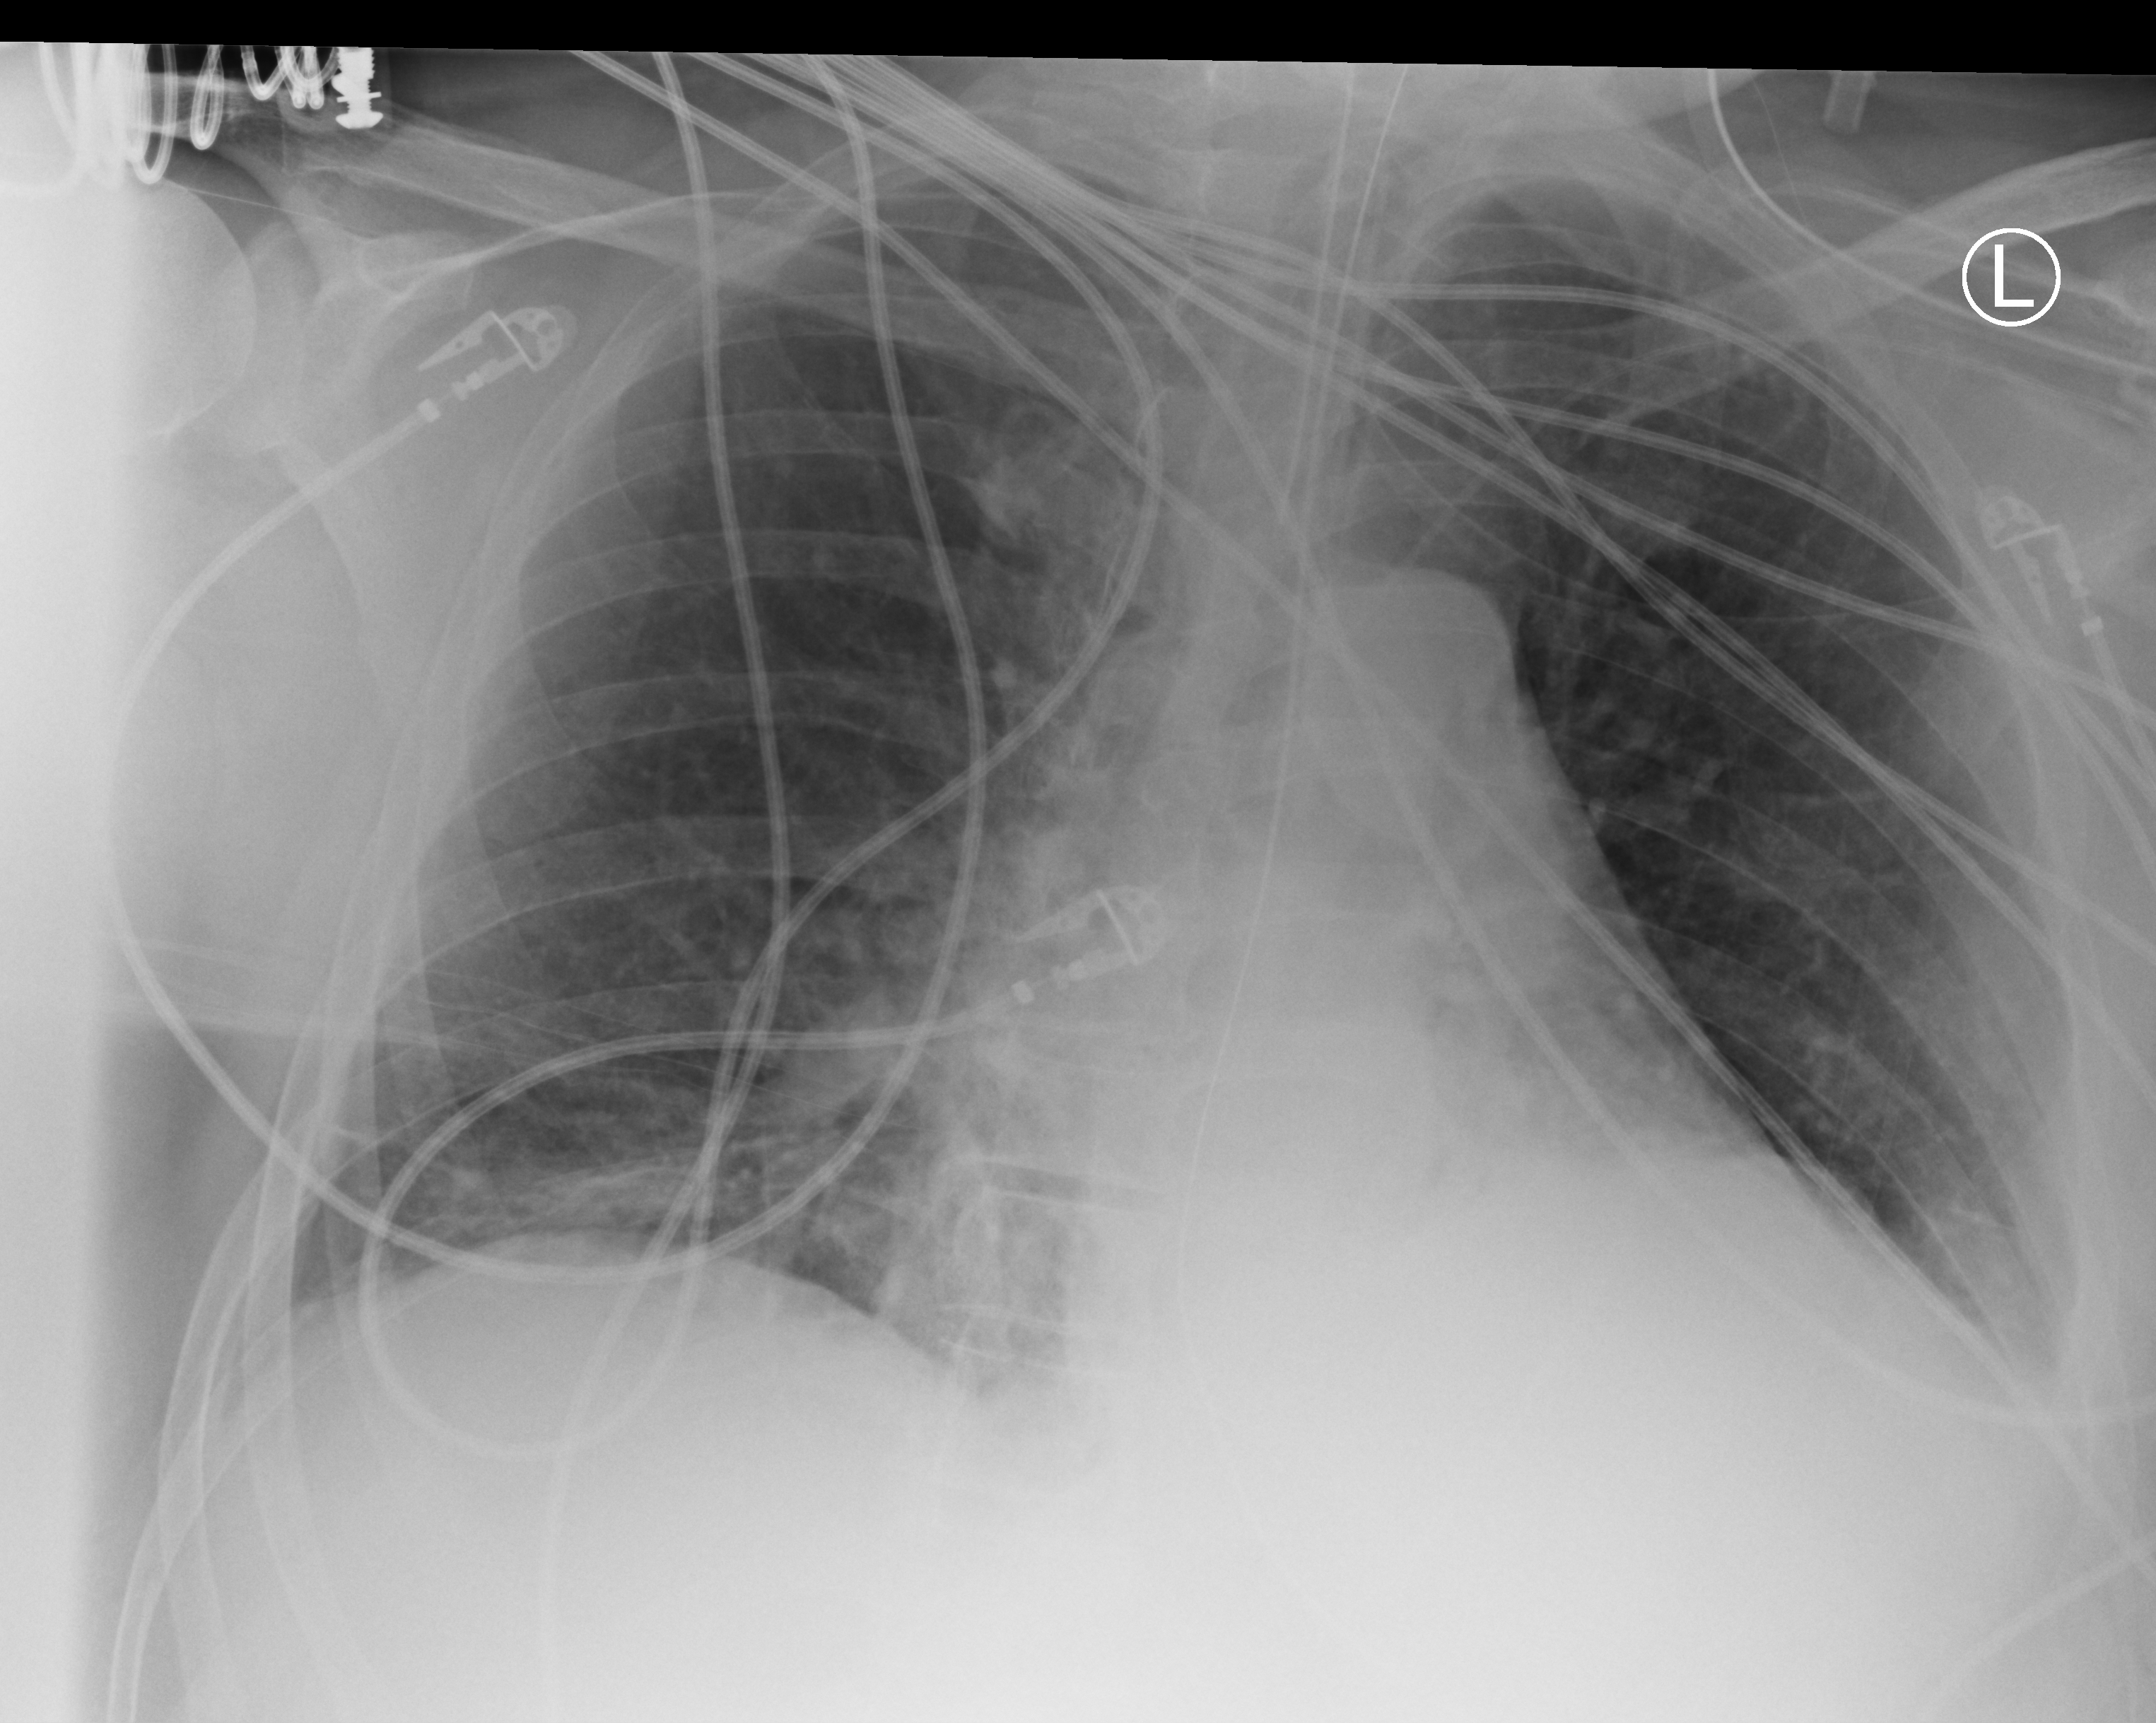
Bedside chest radiograph (computed radiography). Patient hospitalised with COVID-19; male, aged 60–74 years.
From the hospital-stay record, not from the radiograph (when in the stay this image was taken is not recorded): mechanically ventilated during this hospital stay: yes; admitted to intensive care during this hospital stay: yes; chronic kidney disease (admission record): no.